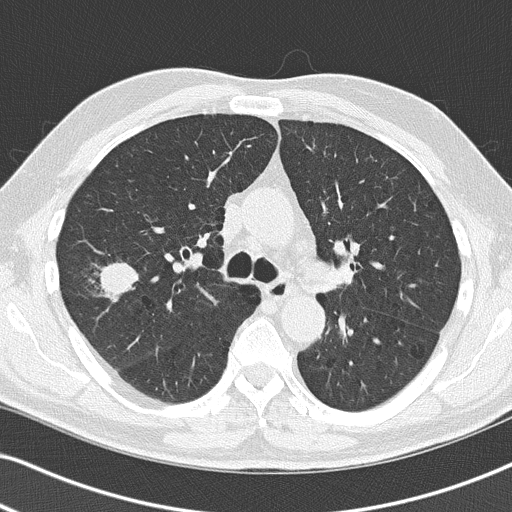
Low-dose screening chest CT, one axial slice; slice 85 of 140 in the series (ordered by position); reconstruction kernel B50f; lung window (W 1500 / L -600 HU); 2 mm slice thickness; 512 × 512 image matrix, field of view 330 × 330 mm.
Structures marked on this image (outlined manually by an expert reader):
- lesion 1 (tumor, upper lobe of right lung): bounding box [x1, y1, x2, y2] px = [99, 263, 138, 297]